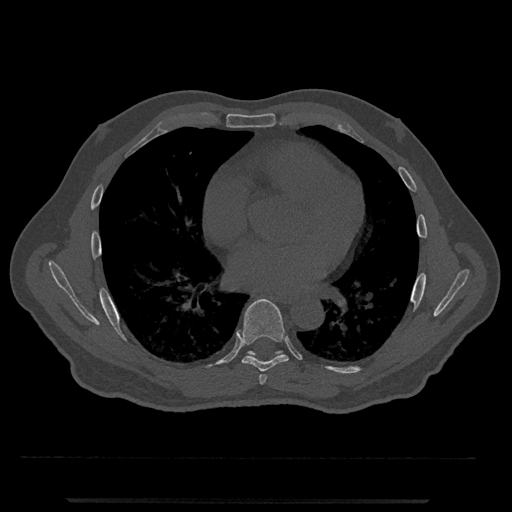
CT including the spine, one axial slice. Slice 675 of 797 in the series (ordered by position). Bone window (W 1800 / L 400 HU). 0.5 mm slice thickness. 512 × 512 image matrix. Male patient, age 63 years. Case-level facts recorded for this patient, not image findings: primary cancer: prostate.
Annotated regions visible in this slice (semi-automatic segmentation, software-assisted and operator-edited):
- T6 vertebra: box from (x=259, y=374) to (x=267, y=385) px
- T7 vertebra: (x=236, y=299)–(x=289, y=372)
- T8 vertebra: (x=247, y=351)–(x=283, y=355)